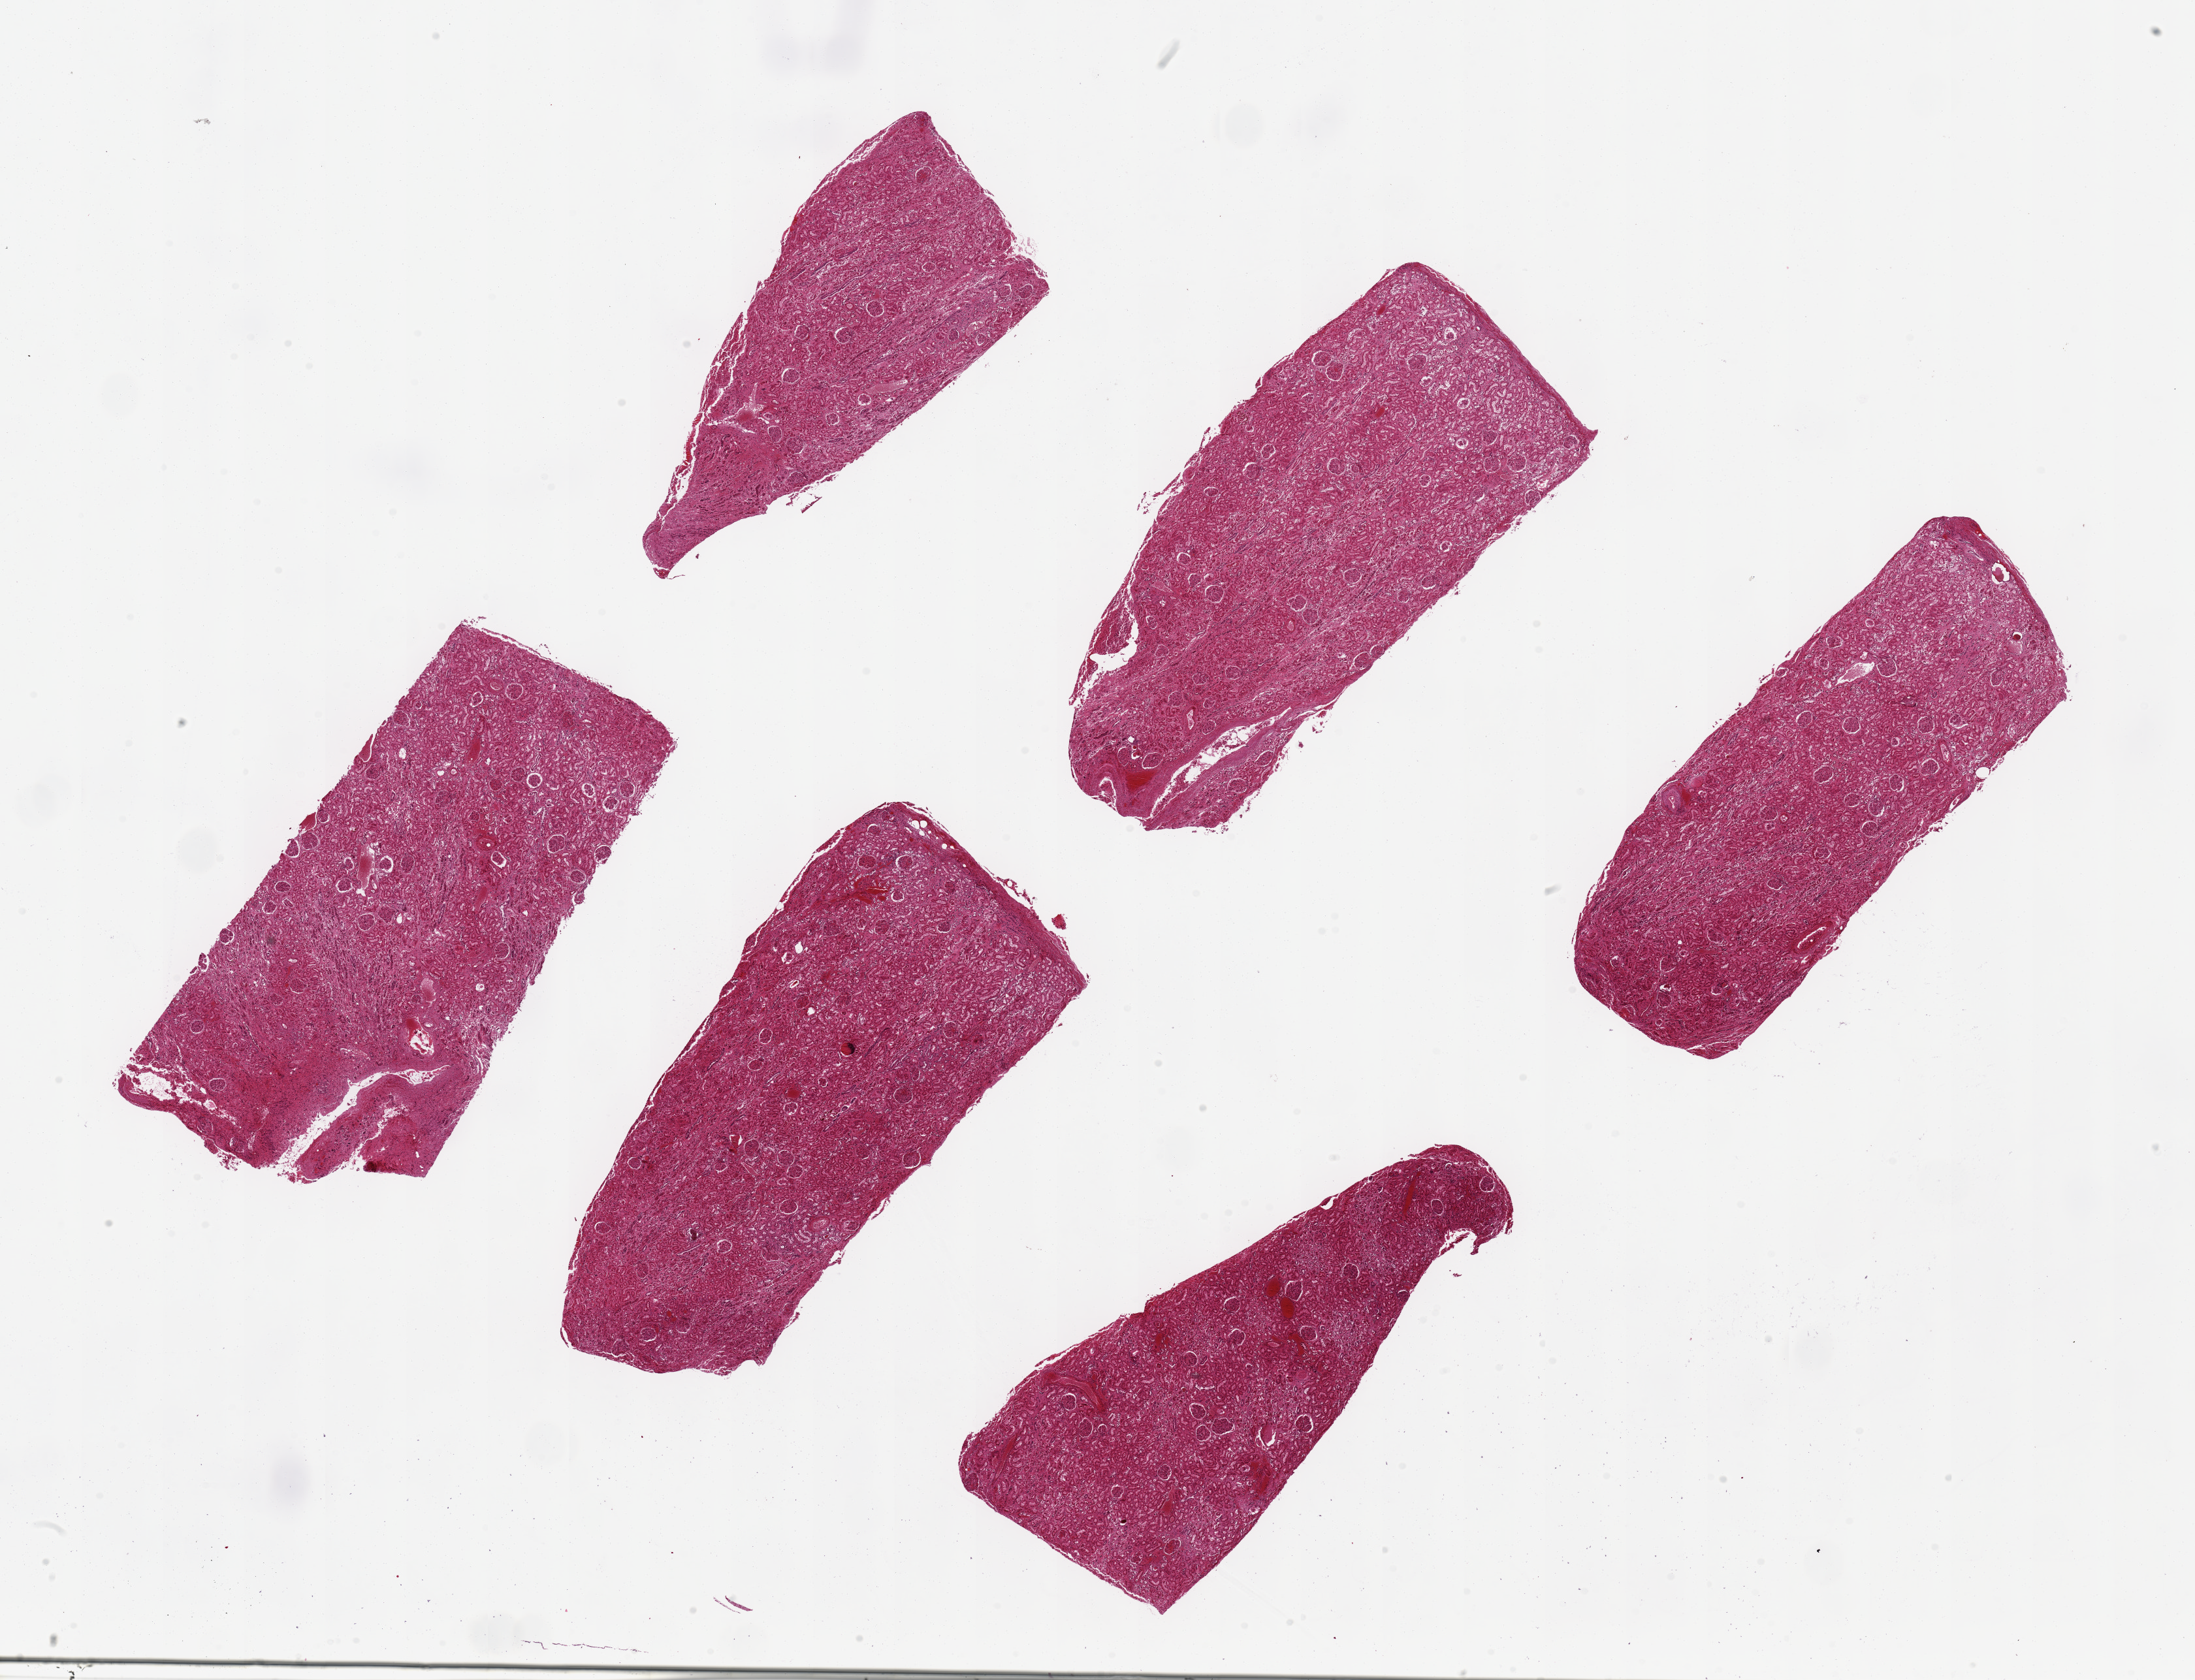
Digitized H&E-stained section, brightfield — whole scanned area (about 26.6 x 20.3 mm, slide scanned at 20x) shown as a low-resolution overview; PAXgene-fixed paraffin-embedded (PFPE) section; target tissue: renal cortex; donor tissue sample. Donor sex: male.
* pathologist's review note for this sample: 6 pieces ~7x3mm. Tubules badly autolyzed